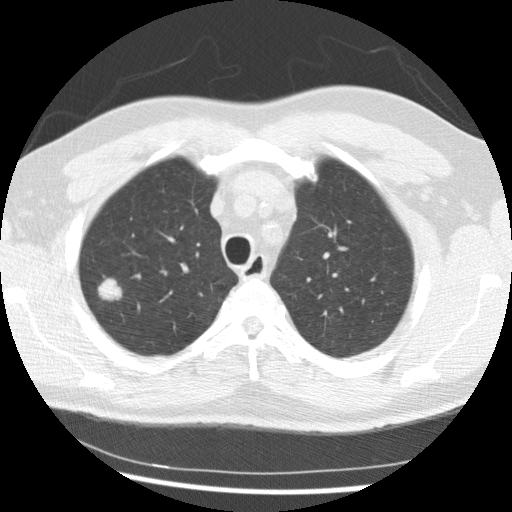
Axial slice from a low-dose chest CT screening exam. First (baseline) screen. Lung window (W 1500 / L -600 HU). 2.5 mm slice thickness. Slice 58 of 265 in the series. Male participant, aged 56 years at enrolment.
Expert-annotated lung lesion, bounding box <78,269,131,315> (left, top, right, bottom; pixels). Reader record for this screening exam (exam-level; its link to the box is not recorded): non-calcified nodule or mass ≥4 mm, right upper lobe, 19 × 15 mm, spiculated (stellate) margins, soft tissue attenuation. Participant outcome: lung cancer diagnosed 291 days after this screen — non-small cell carcinoma, right upper lobe, poorly differentiated (G3), stage IIIB (AJCC 6th edition), 20 mm at pathology.